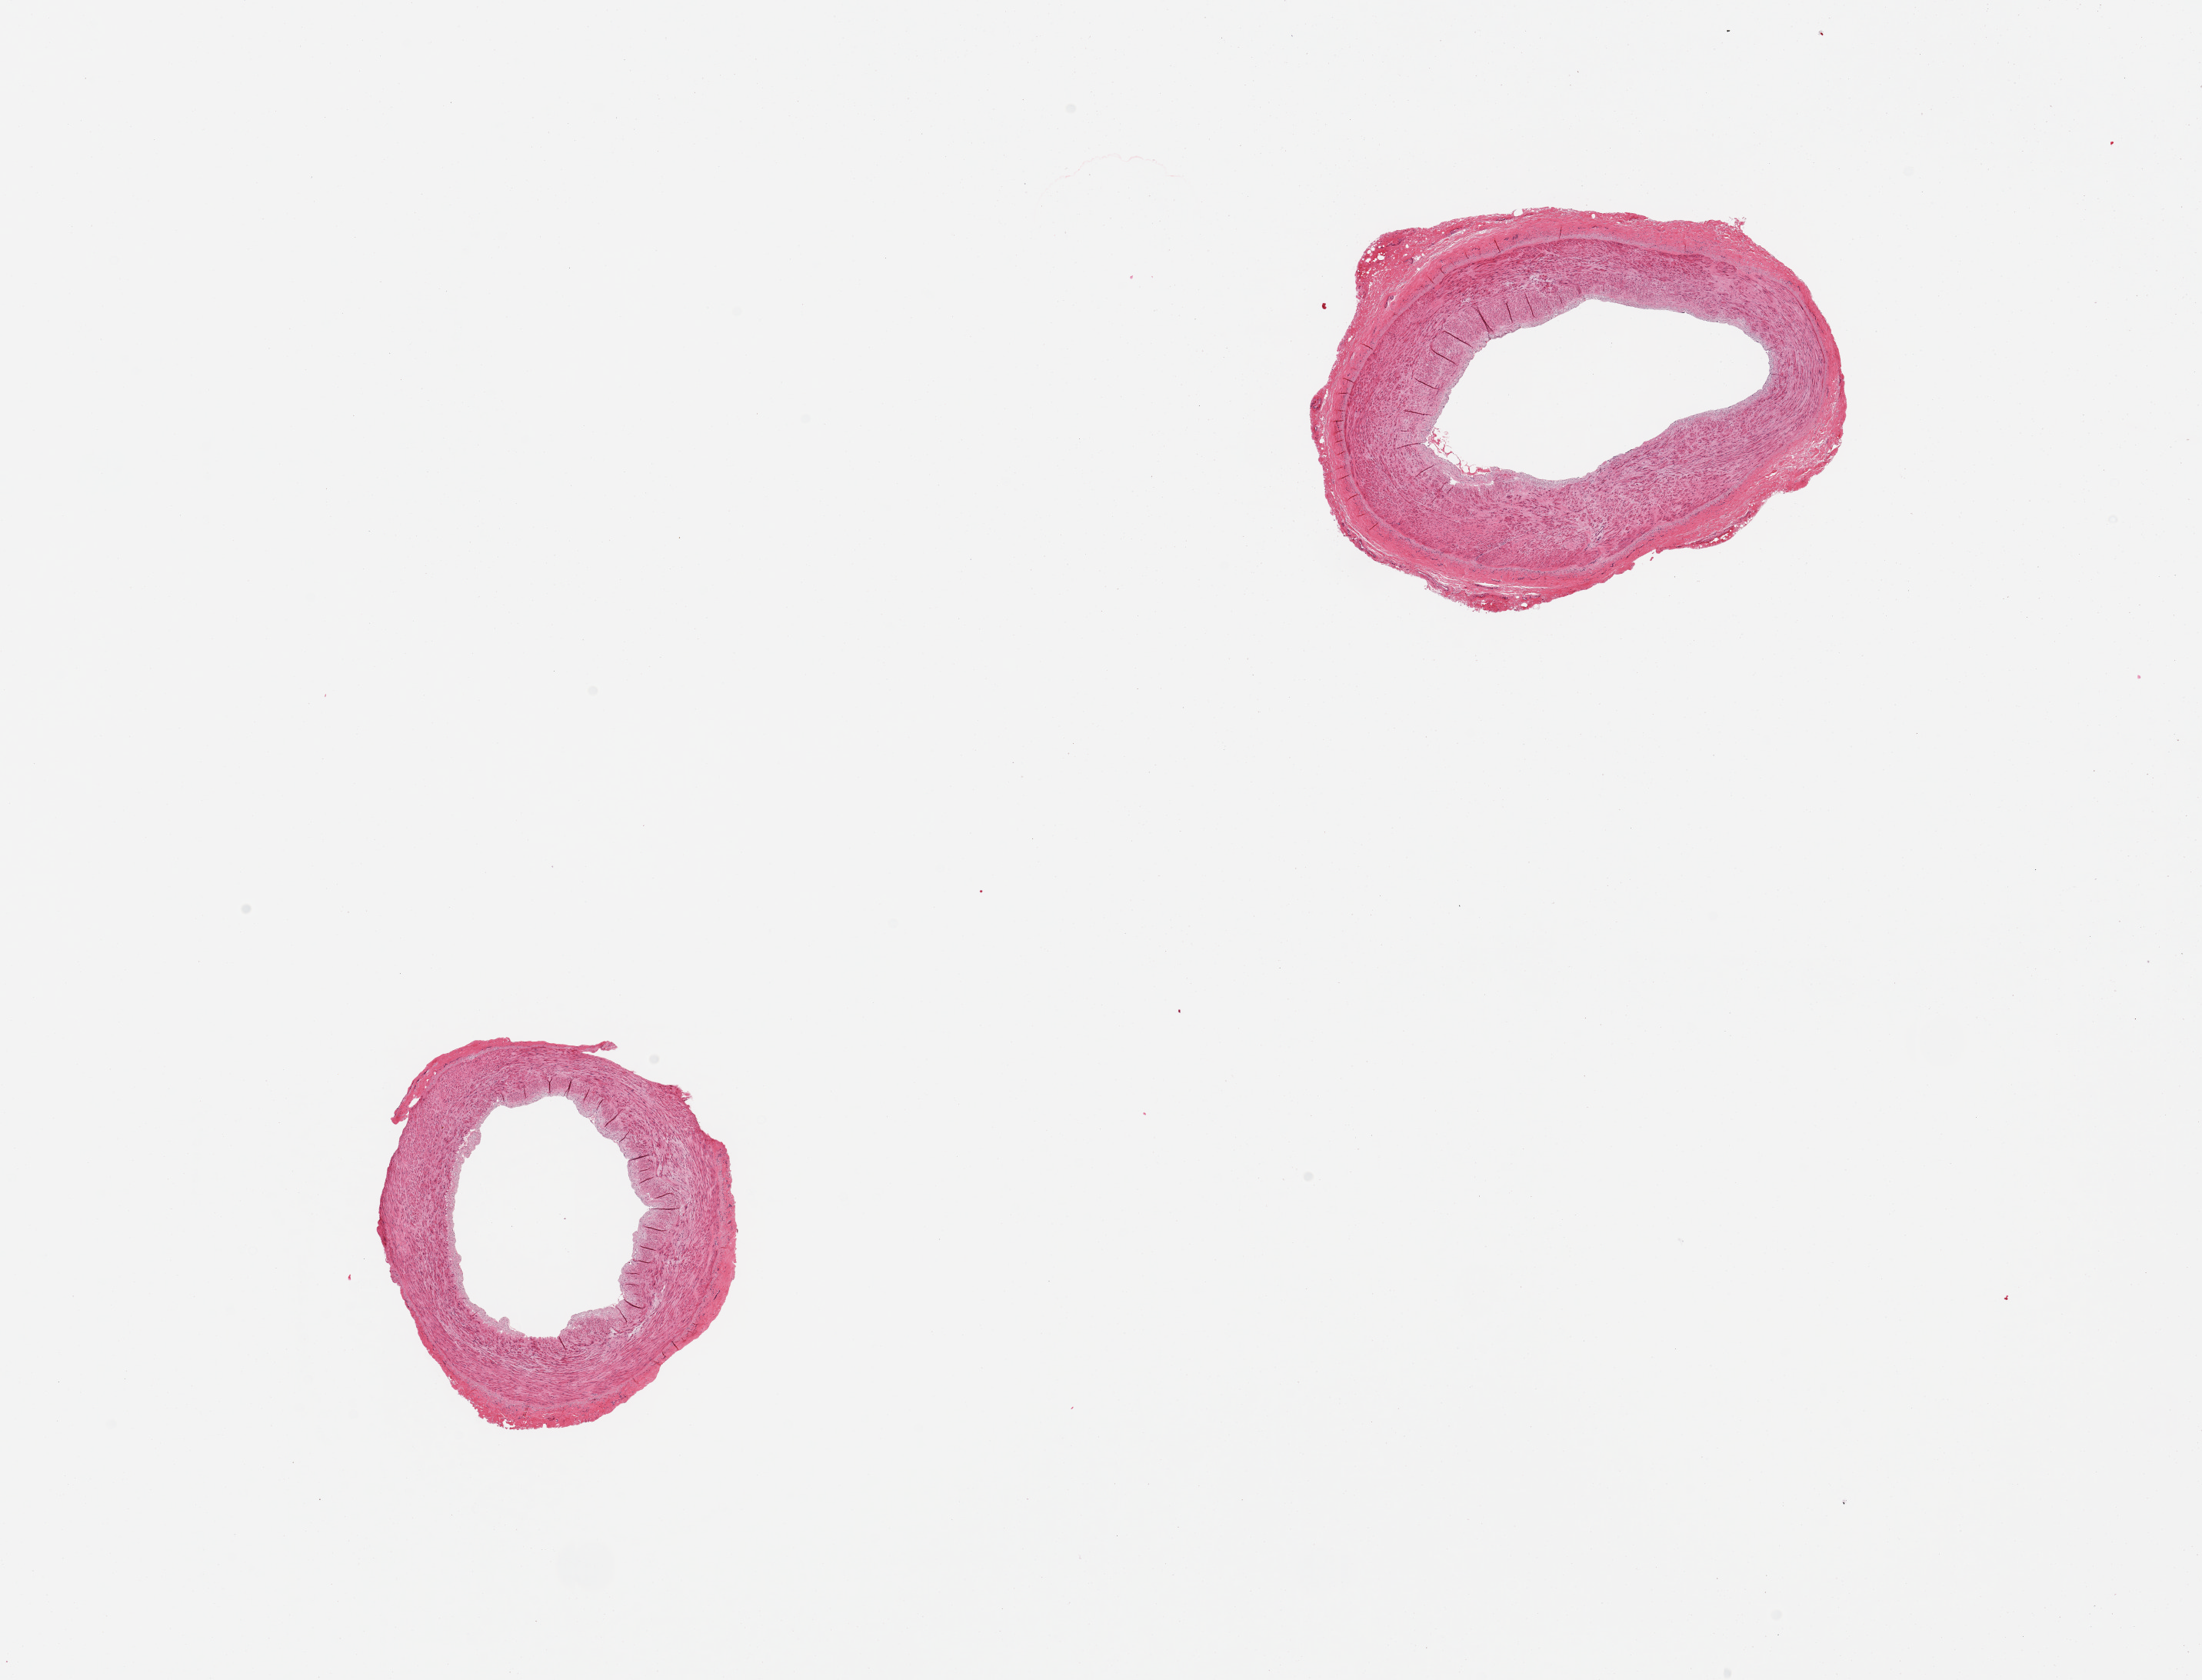
Digitized hematoxylin and eosin (H&E)-stained section, brightfield, a low-resolution overview of the entire scanned area, about 22.6 x 17.3 mm. PAXgene-fixed paraffin-embedded (PFPE) section. Target tissue: tibial artery. Tissue donor sample. Donor: female.
• pathologist's review note for this sample: 2 pieces. Well trimmed